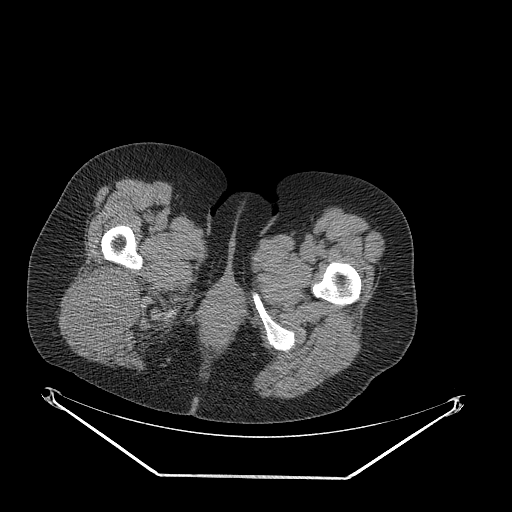
CT of an extremity soft-tissue mass (from a PET/CT study), one axial slice; position 53 of 257 along the scan axis; reconstruction kernel STANDARD; 140 kVp; soft-tissue window (W 400 / L 40 HU); 512 × 512 image matrix. Female patient. Case-level facts recorded for this patient, not image findings: histological type: synovial sarcoma; grade: intermediate; site of the primary tumour: right buttock.
Annotated regions visible in this slice (expert contour drawn on MRI and transferred to this co-registered scan by the dataset authors):
- gross tumour volume including surrounding oedema: bounding box <71,263,145,353> (left, top, right, bottom; pixels)
- gross tumour volume (mass): <71,263,145,350>